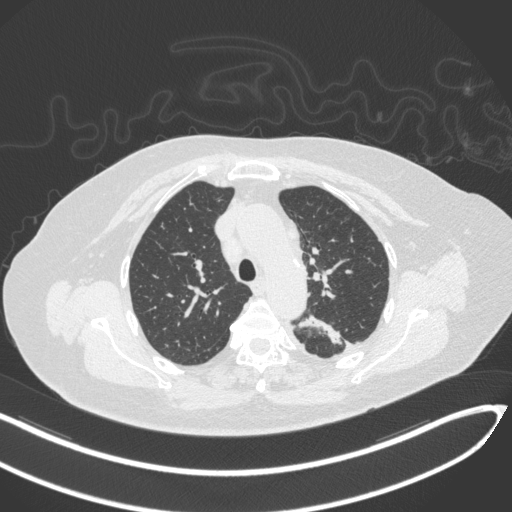
Chest CT, one axial slice. Position 229 of 270 along the scan axis. 120 kVp. Lung window (W 1500 / L -600 HU). 1 mm slice thickness. 512 × 512 image matrix, field of view 400 × 400 mm. Patient: female, 76 years. Case-level facts recorded for this patient, not image findings: clinical TNM (as recorded): T1c N0 M0.
Outlined on this slice (rectangle marked by the reading radiologist):
- lung tumour (recorded histology: adenocarcinoma): box from (x=298, y=311) to (x=350, y=346) px